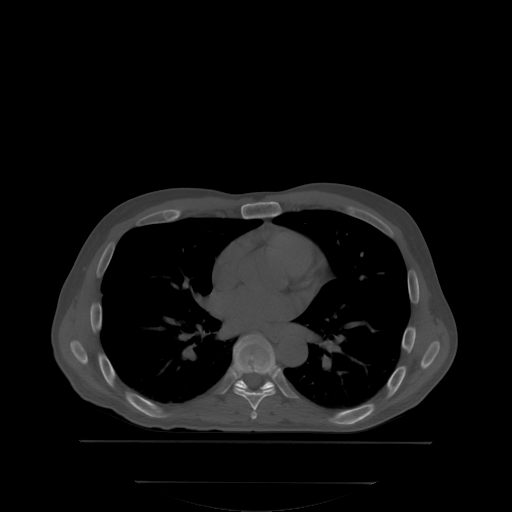
CT including the spine, one axial slice; position 223 of 350 along the scan axis; bone window (W 1800 / L 400 HU); 512 × 512 image matrix, field of view 500 × 500 mm. Patient: male, 58 years. Case-level facts recorded for this patient, not image findings: primary cancer: prostate; vertebrae with lytic lesions (as recorded): L1.
Structures marked on this image (semi-automatically segmented with operator editing):
- T6 vertebra: bounding box <252,409,256,417> (left, top, right, bottom; pixels)
- T7 vertebra: <234,388,275,409>
- T8 vertebra: <233,335,276,390>